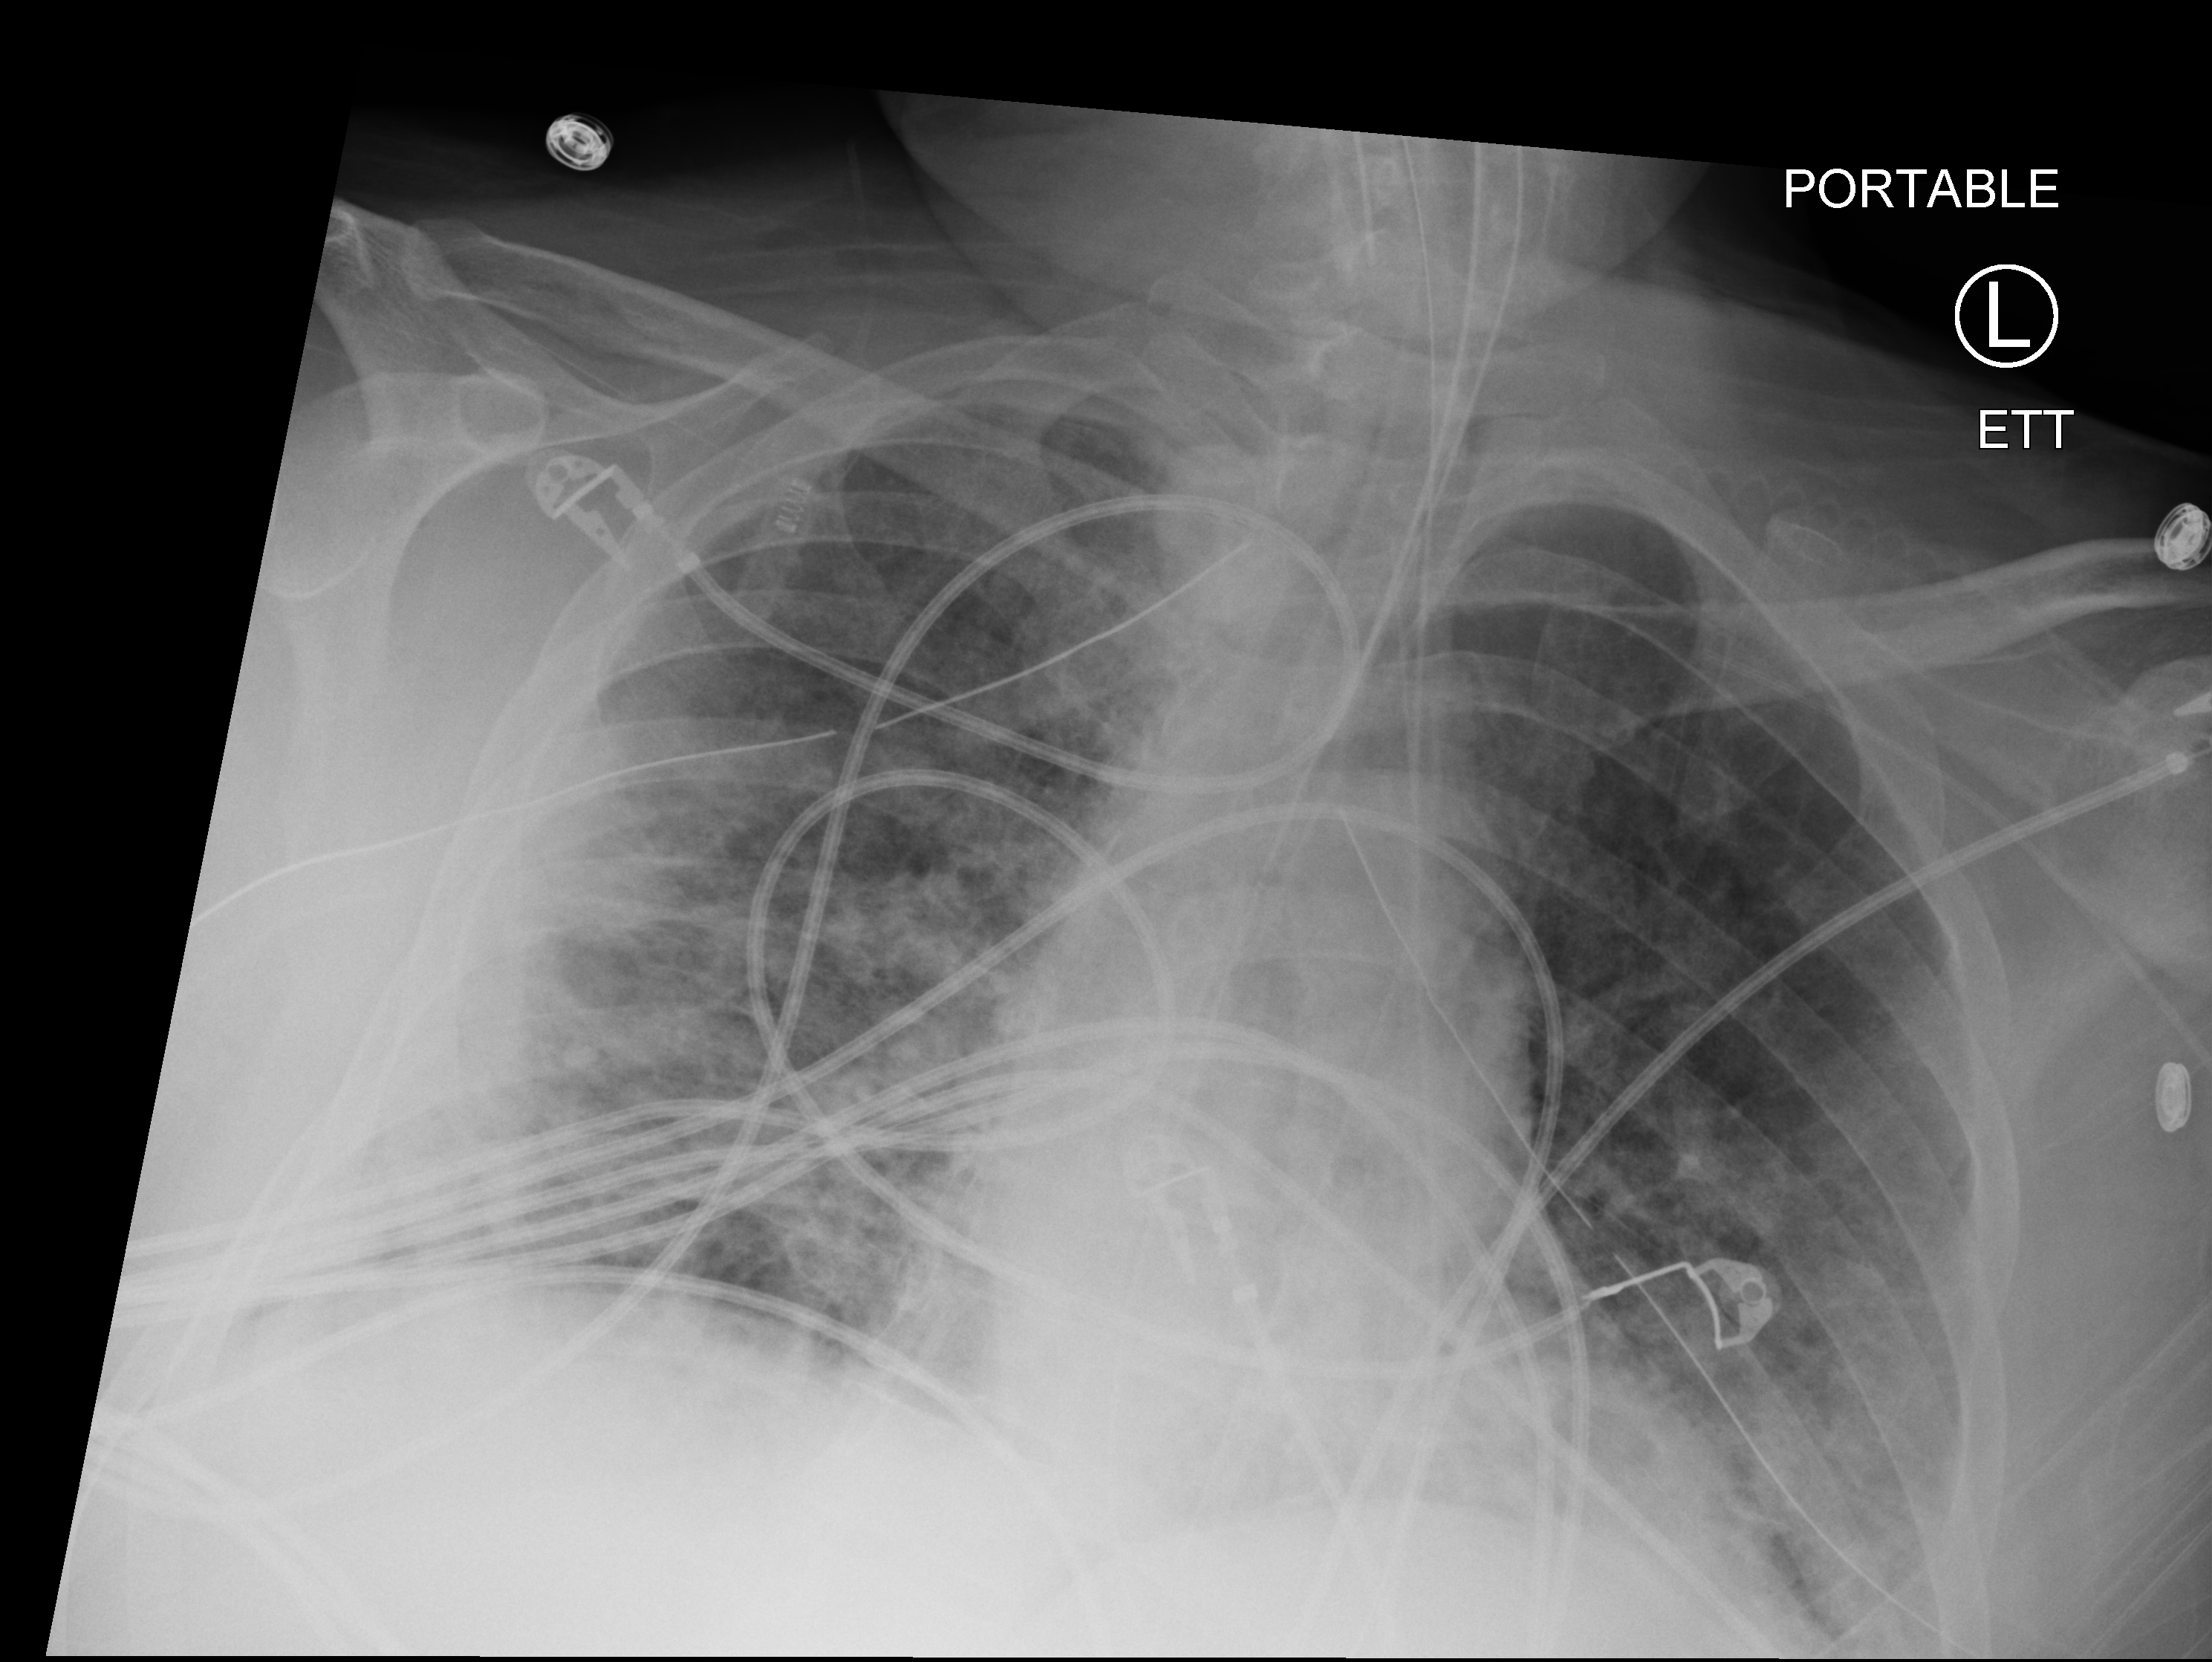
Portable chest radiograph, anteroposterior (AP) projection. Male patient hospitalised with COVID-19, age 18–59 years.
Admission-level facts for this patient (not findings on this image; timing relative to this image not recorded):
- mechanically ventilated during this hospital stay: yes